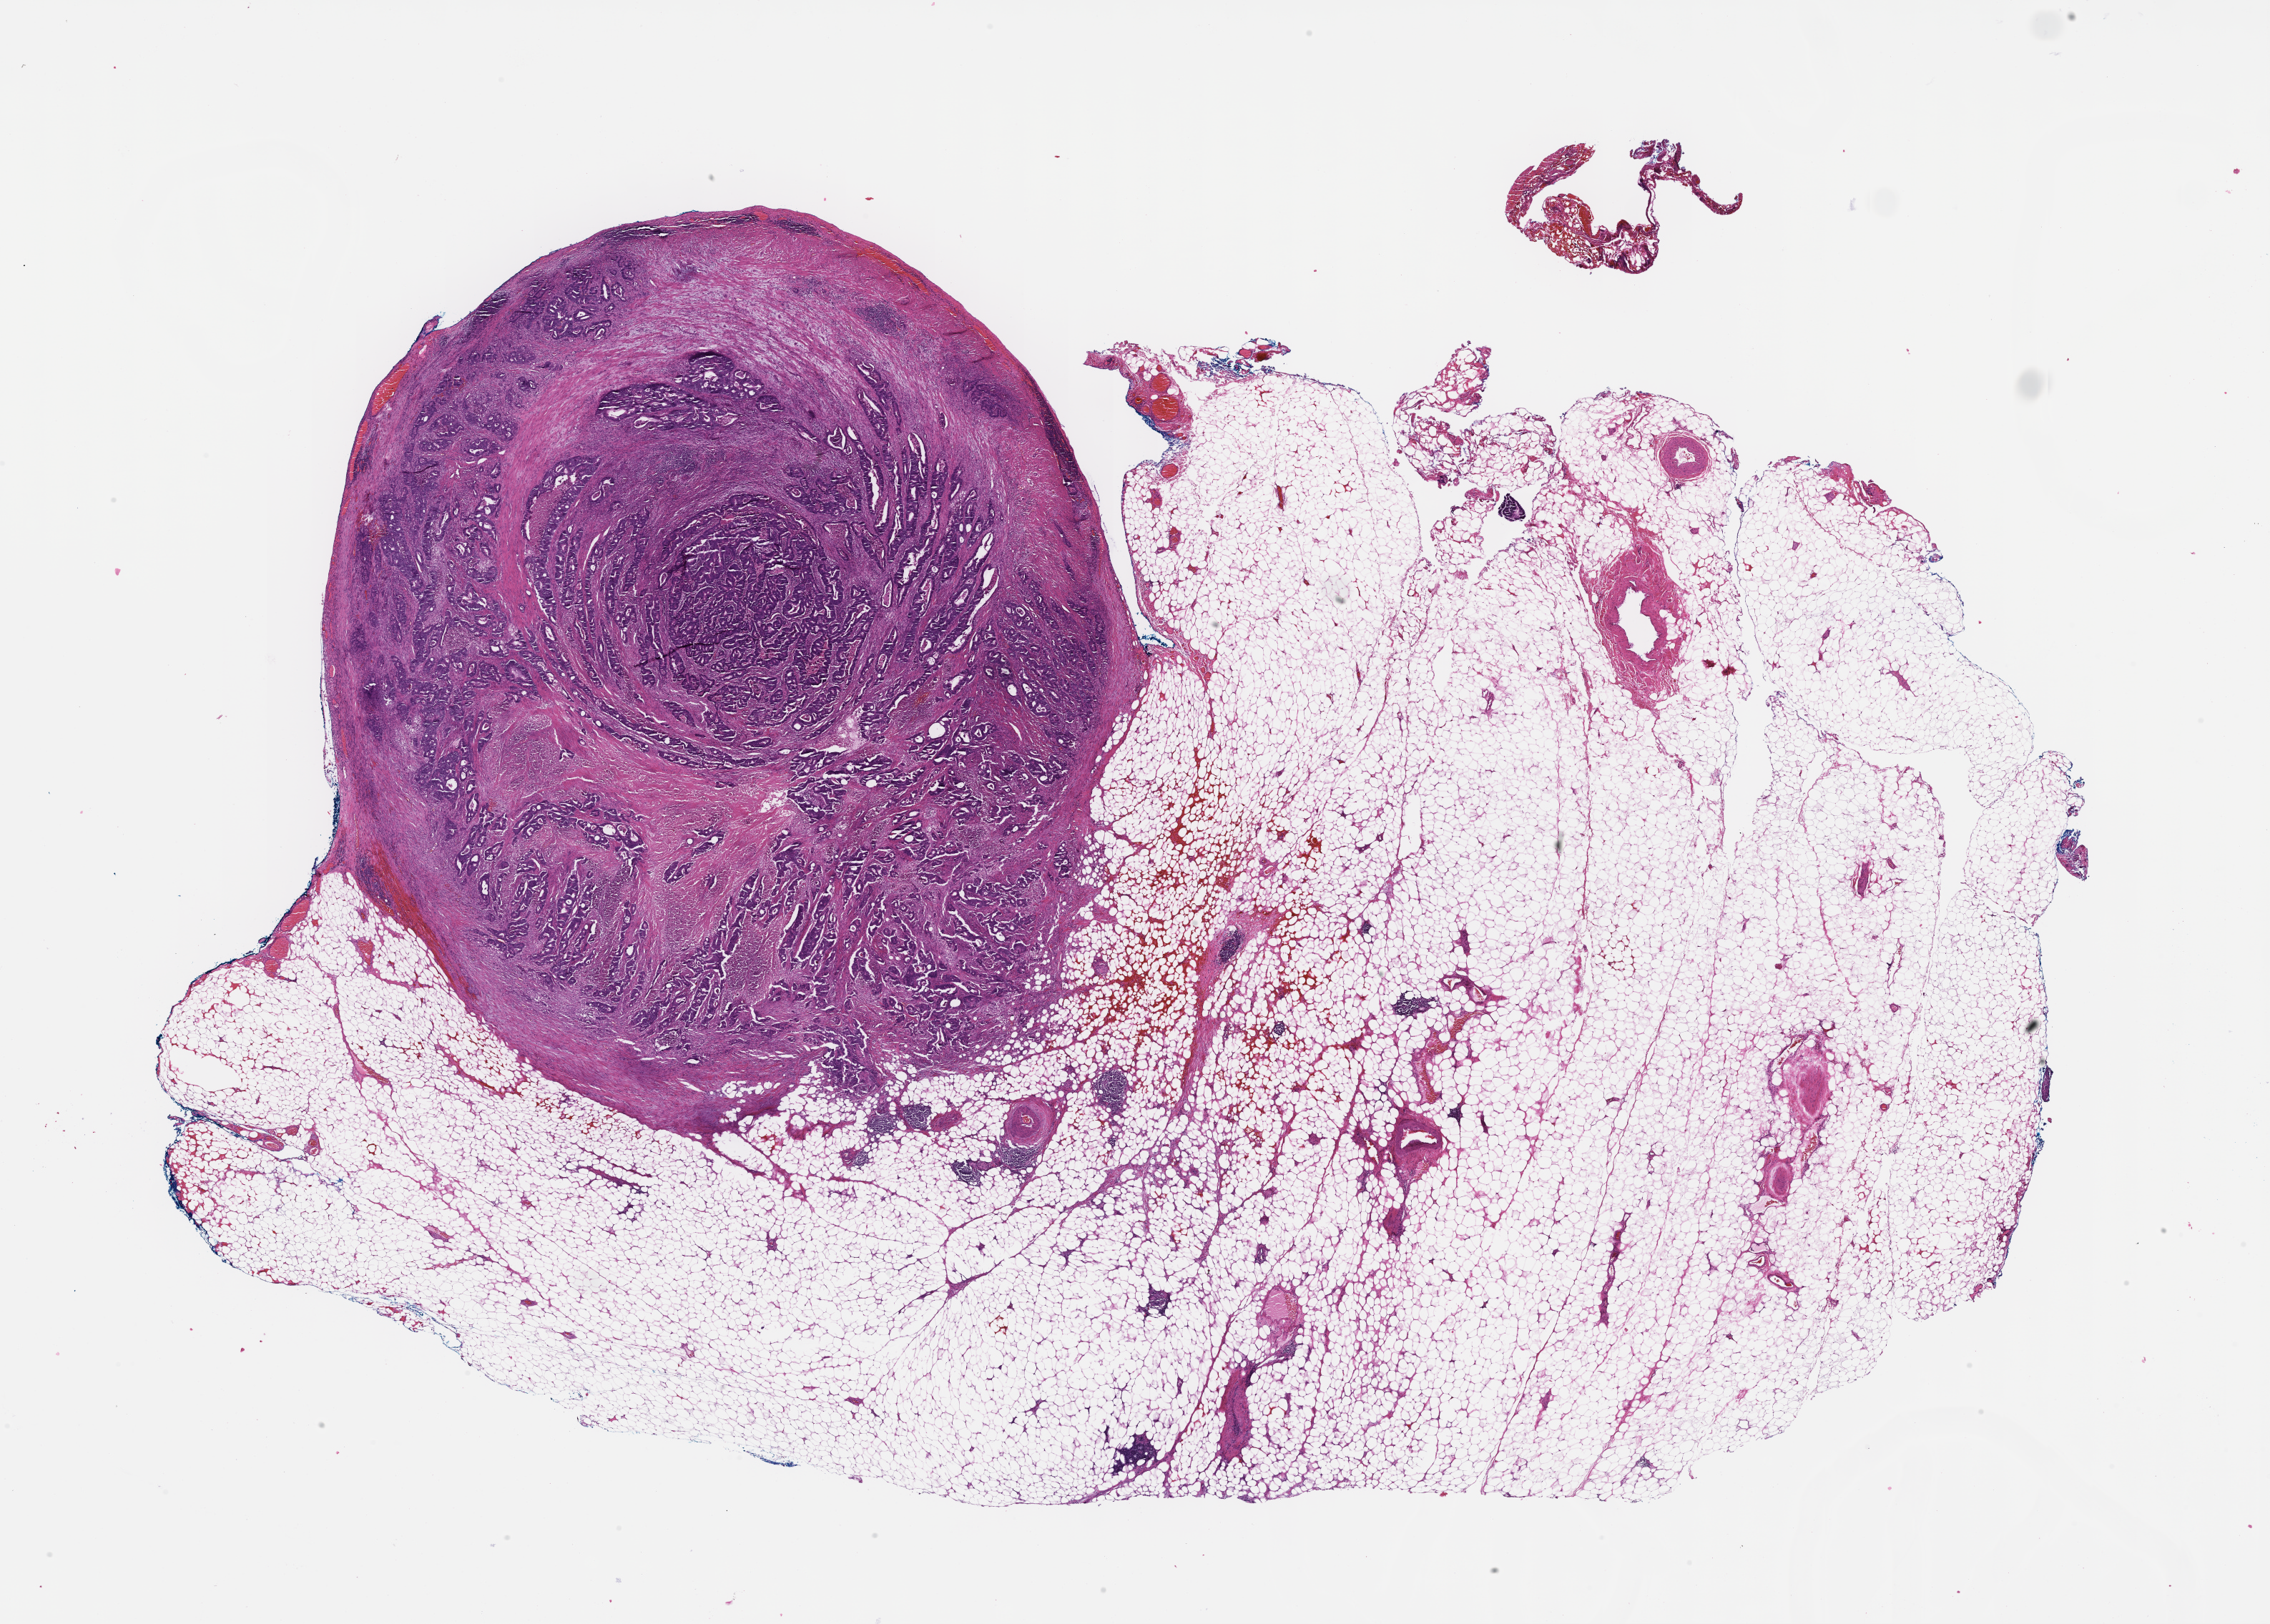
Digitized hematoxylin and eosin (H&E)-stained section, low-resolution overview of the scanned area, about 25.6 x 18.3 mm. FFPE section. Patient sex: male.
• this section: metastatic tumor tissue
• primary diagnosis of the patient: Colorectal Carcinoma